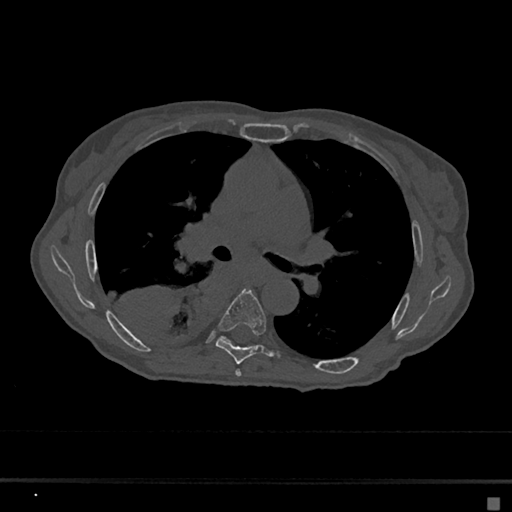
CT including the spine, one axial slice. Position 415 of 797 along the scan axis. Bone window (W 1800 / L 400 HU). 512 × 512 image matrix, field of view 360 × 360 mm. Female patient, age 68 years. From the clinical record (not read from this slice): primary cancer: renal.
Annotated regions visible in this slice (semi-automatic segmentation, software-assisted and operator-edited):
- T5 vertebra: bounding box <235,370,242,377> (left, top, right, bottom; pixels)
- T6 vertebra: <216,289,280,364>